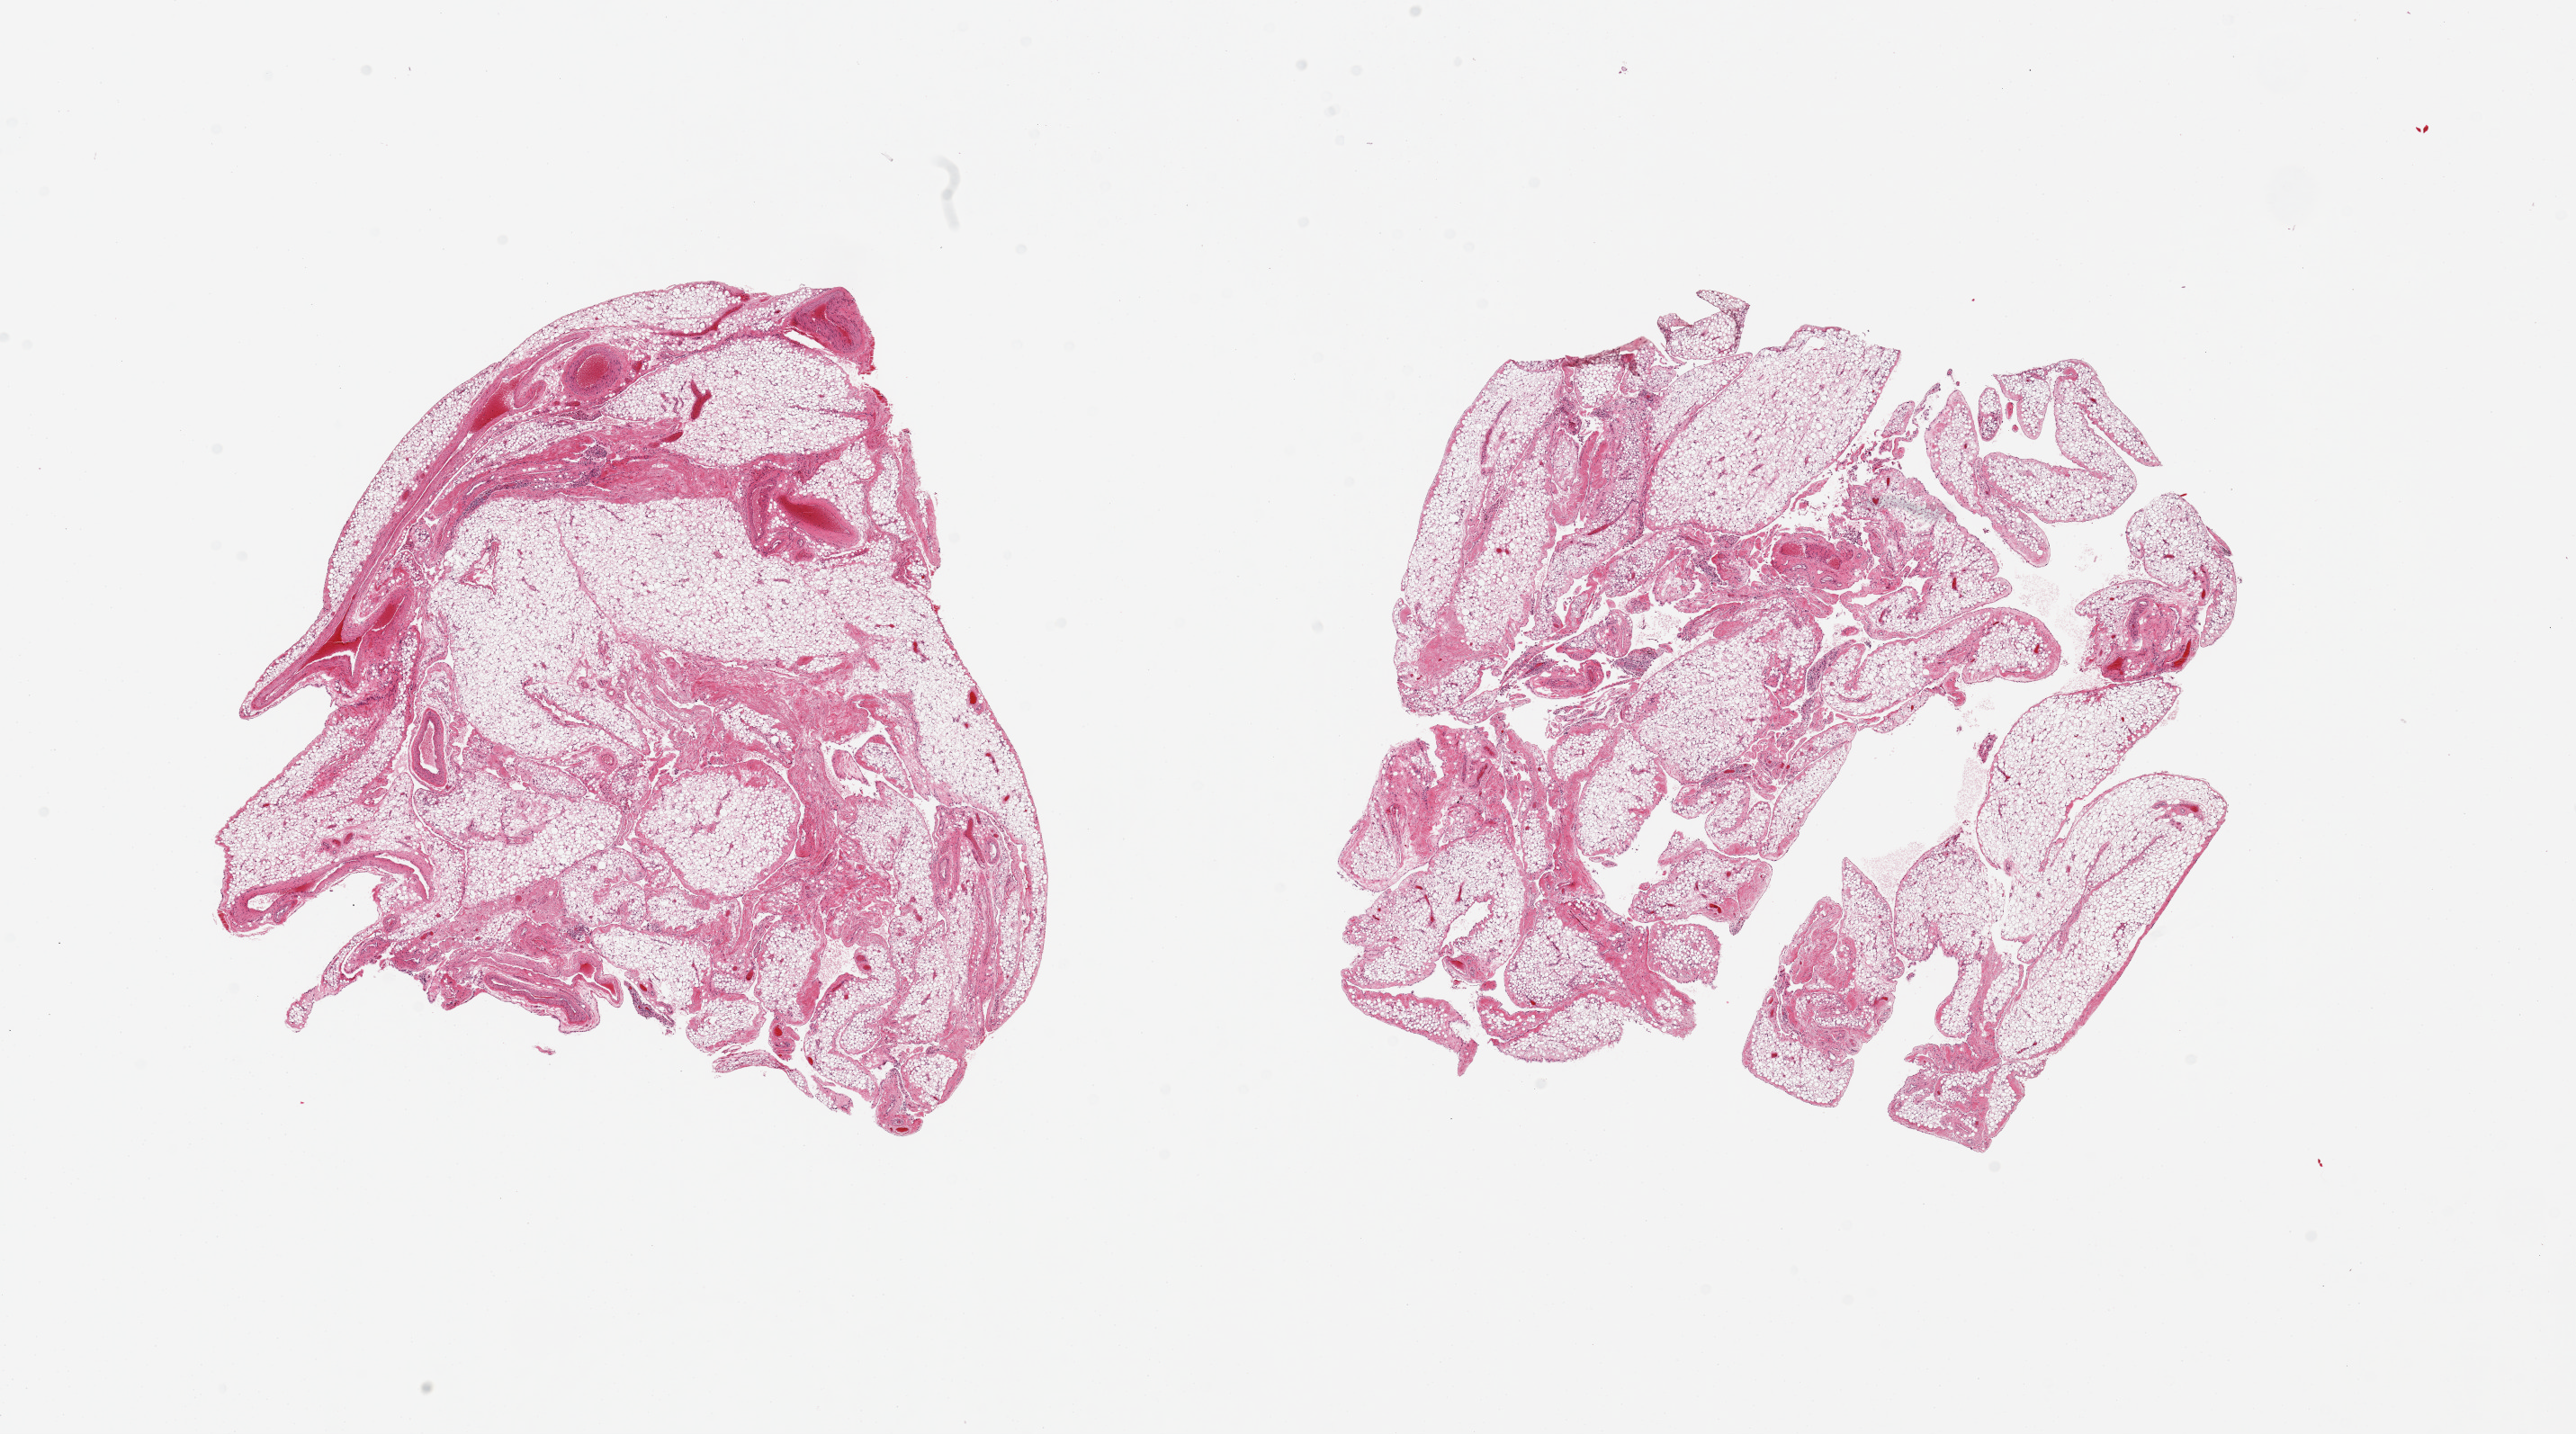
H&E whole-slide image — whole scanned area (about 22.6 x 12.6 mm, from a 20x scan) shown as a low-resolution overview; PAXgene-fixed paraffin-embedded (PFPE) section; target tissue: omentum; donor tissue sample.
* reviewer comment on this tissue sample: 2 pieces; ~40% fibrovascular tissue with several prominent vessels